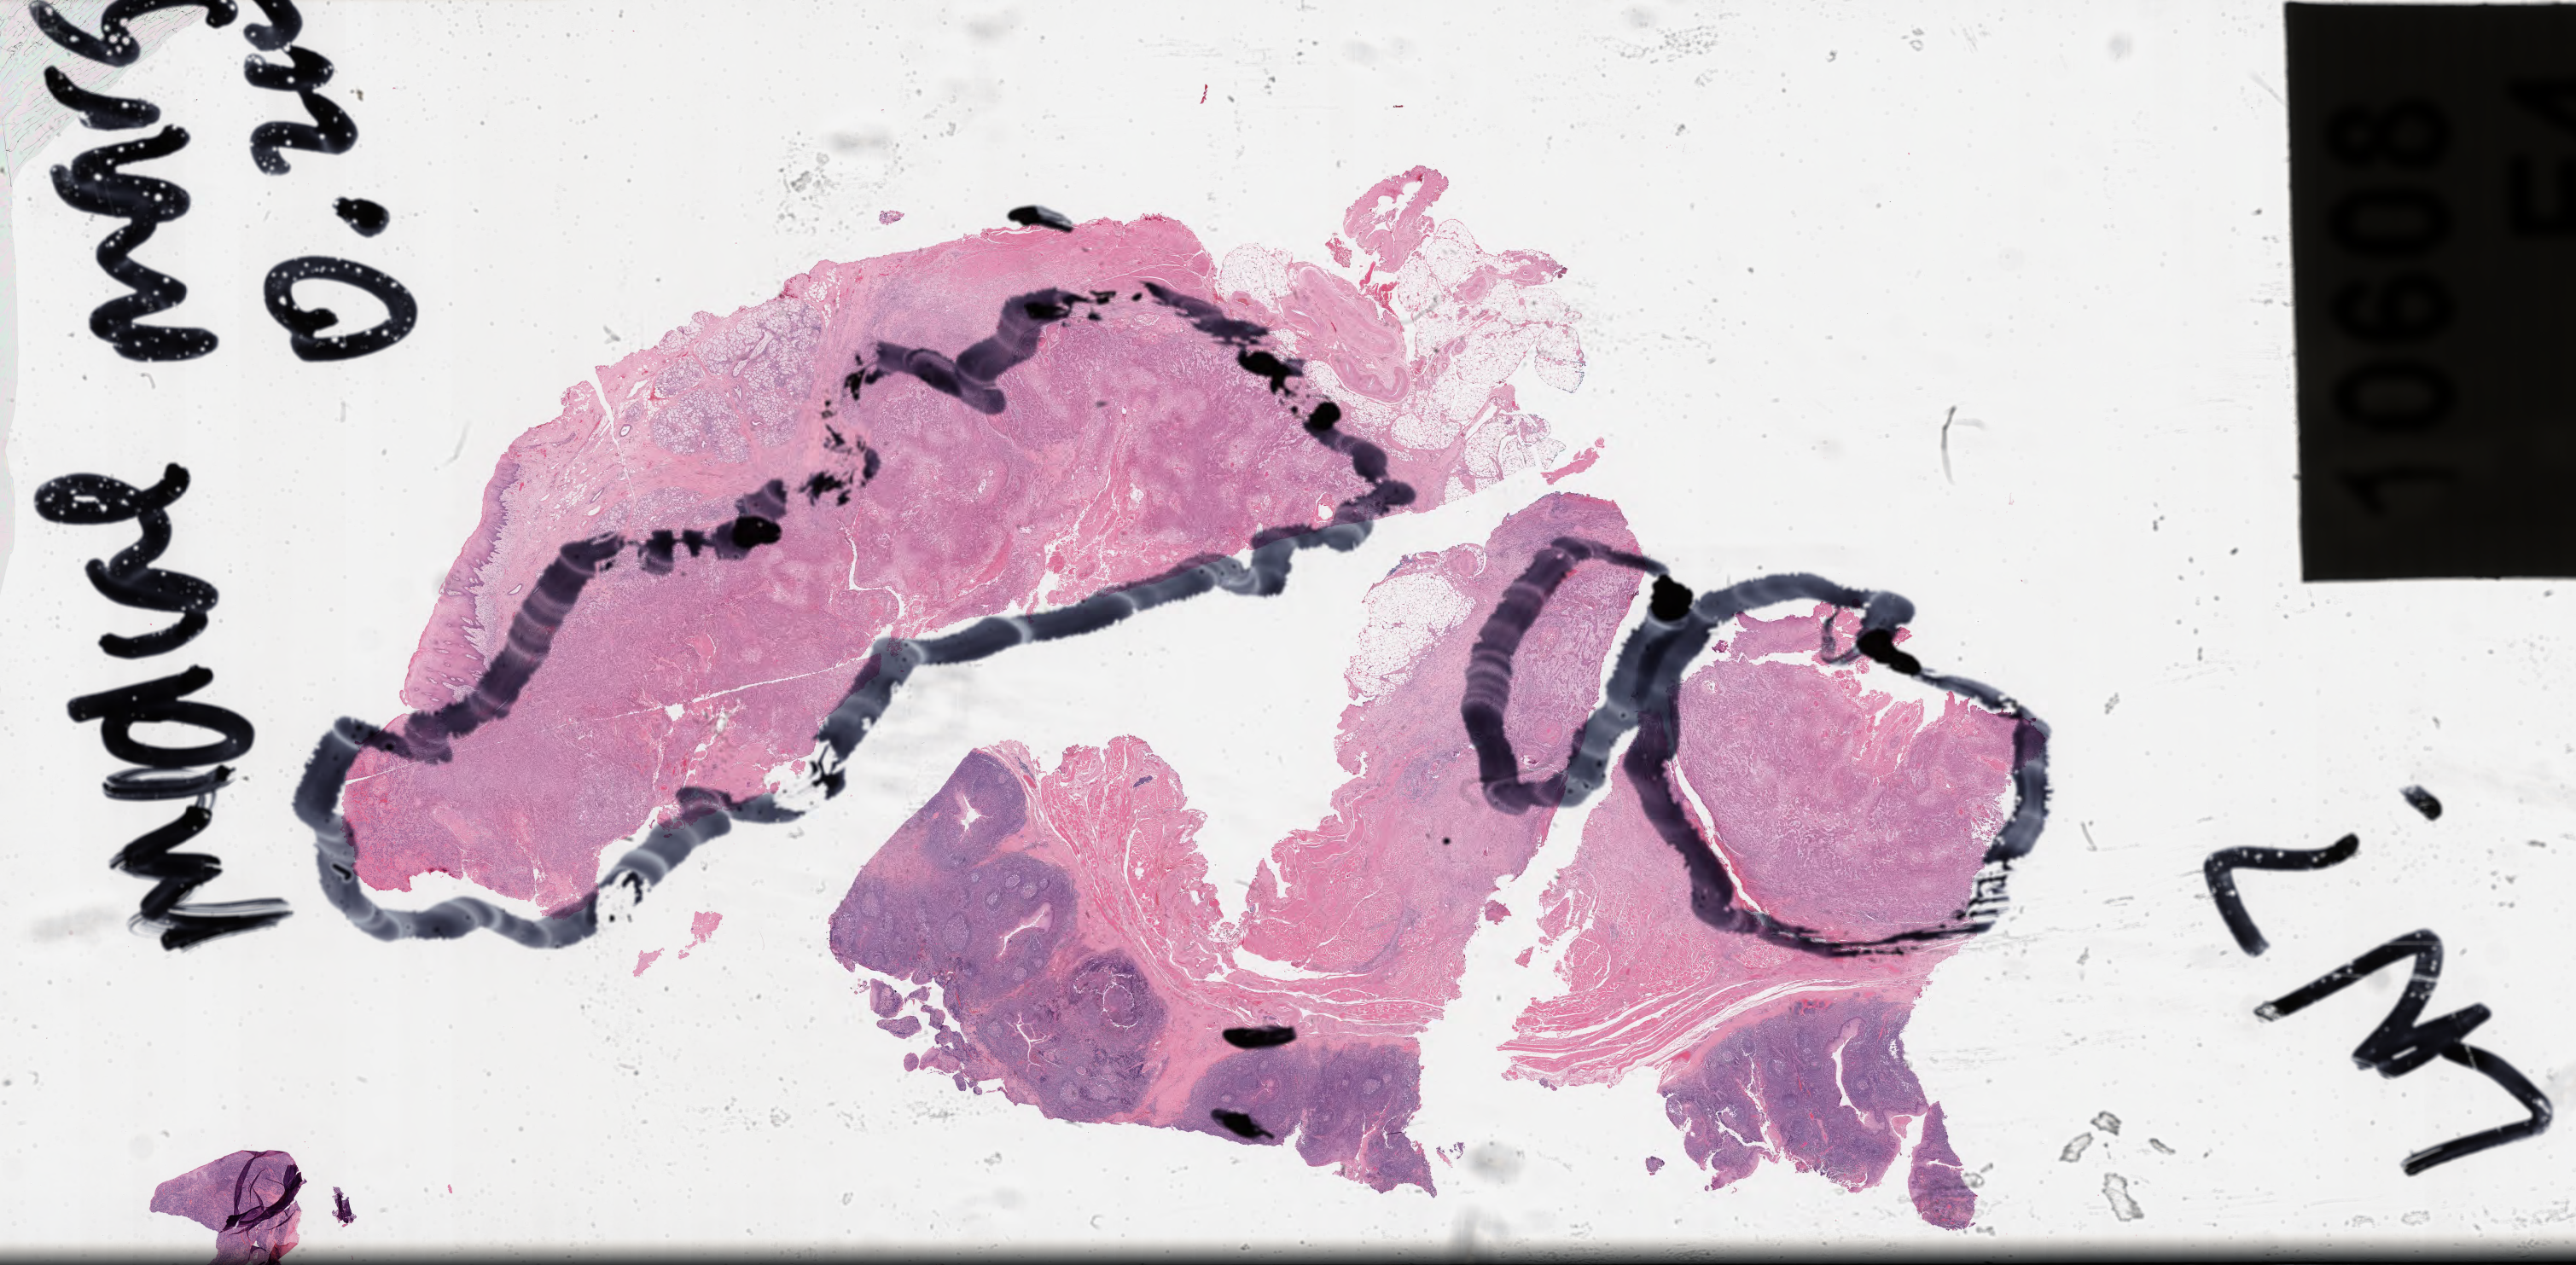
Digitized H&E-stained tissue section (whole slide) — a low-resolution overview of the entire scanned area, about 47.5 x 23.3 mm (from a 40x scan). FFPE section. Sample: primary tumour, head and neck. Male patient; age at initial diagnosis 49 years. Histologic grade: G2 (moderately differentiated).
TNM: T3 N2 MX. Diagnosis: Squamous cell carcinoma, keratinizing, NOS (mouth, NOS). AJCC pathologic stage: IVA (6th edition).